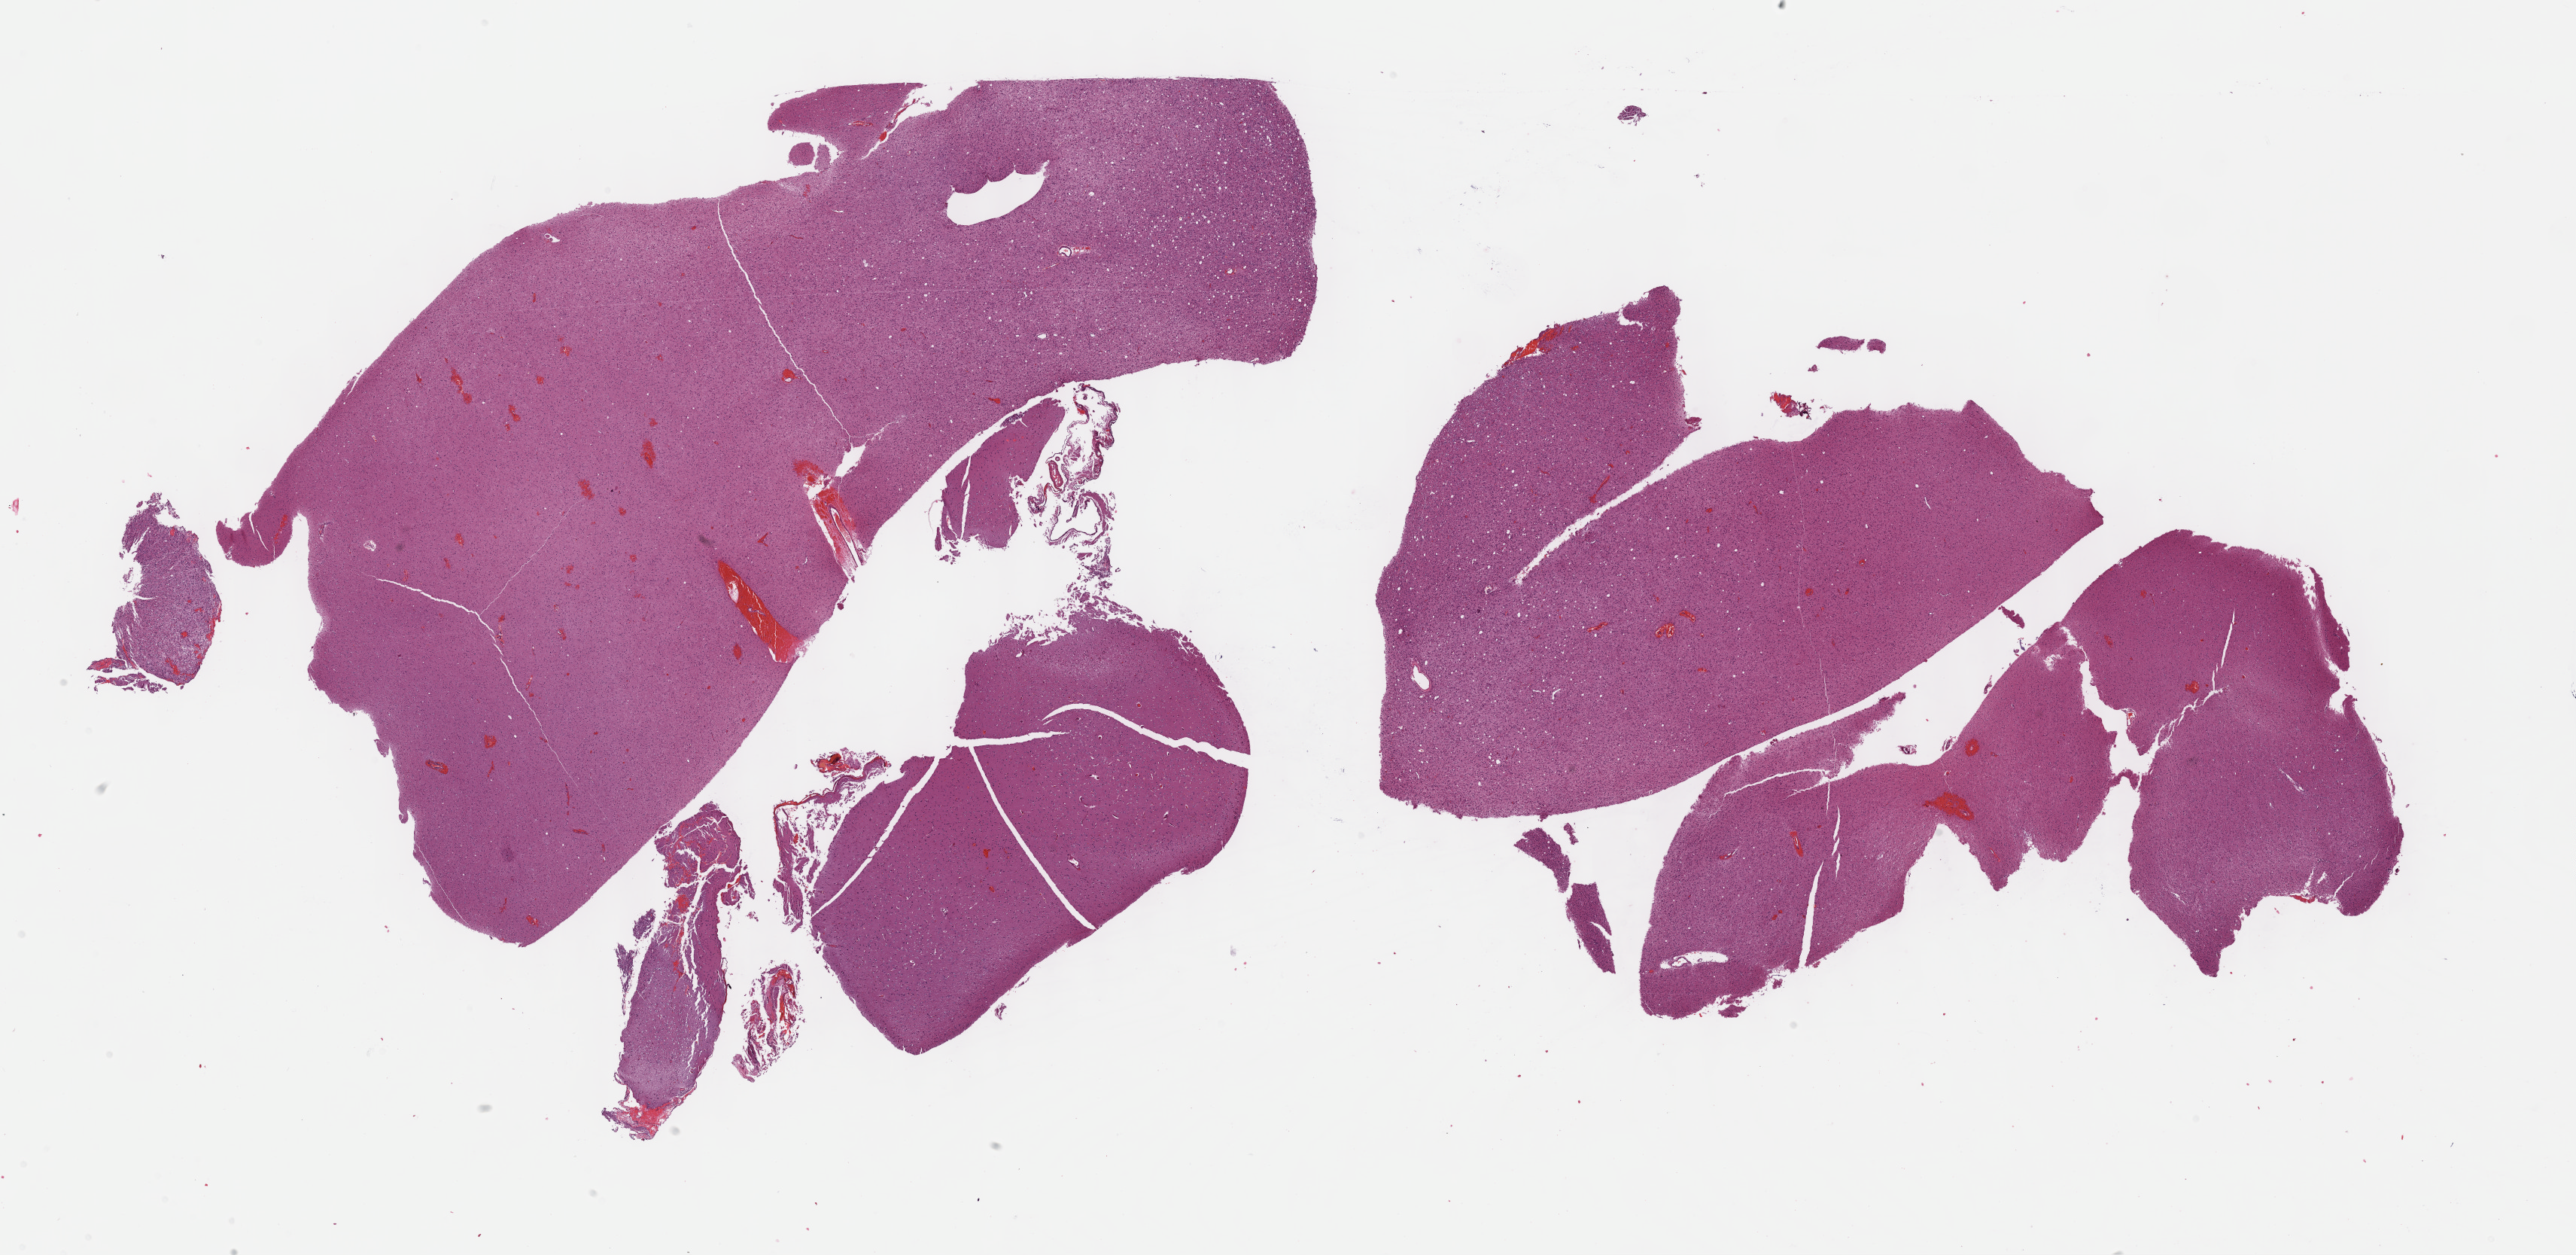
Hematoxylin and eosin (H&E) stained whole-slide image, whole scanned area (about 27.7 x 13.5 mm, slide scanned at 40x) shown as a low-resolution overview; formalin-fixed paraffin-embedded (FFPE) diagnostic section; primary tumour sample from the brain. Female, age 25 years at initial diagnosis. Histologic grade: G2 (moderately differentiated).
• diagnosis: Mixed glioma (cerebrum)